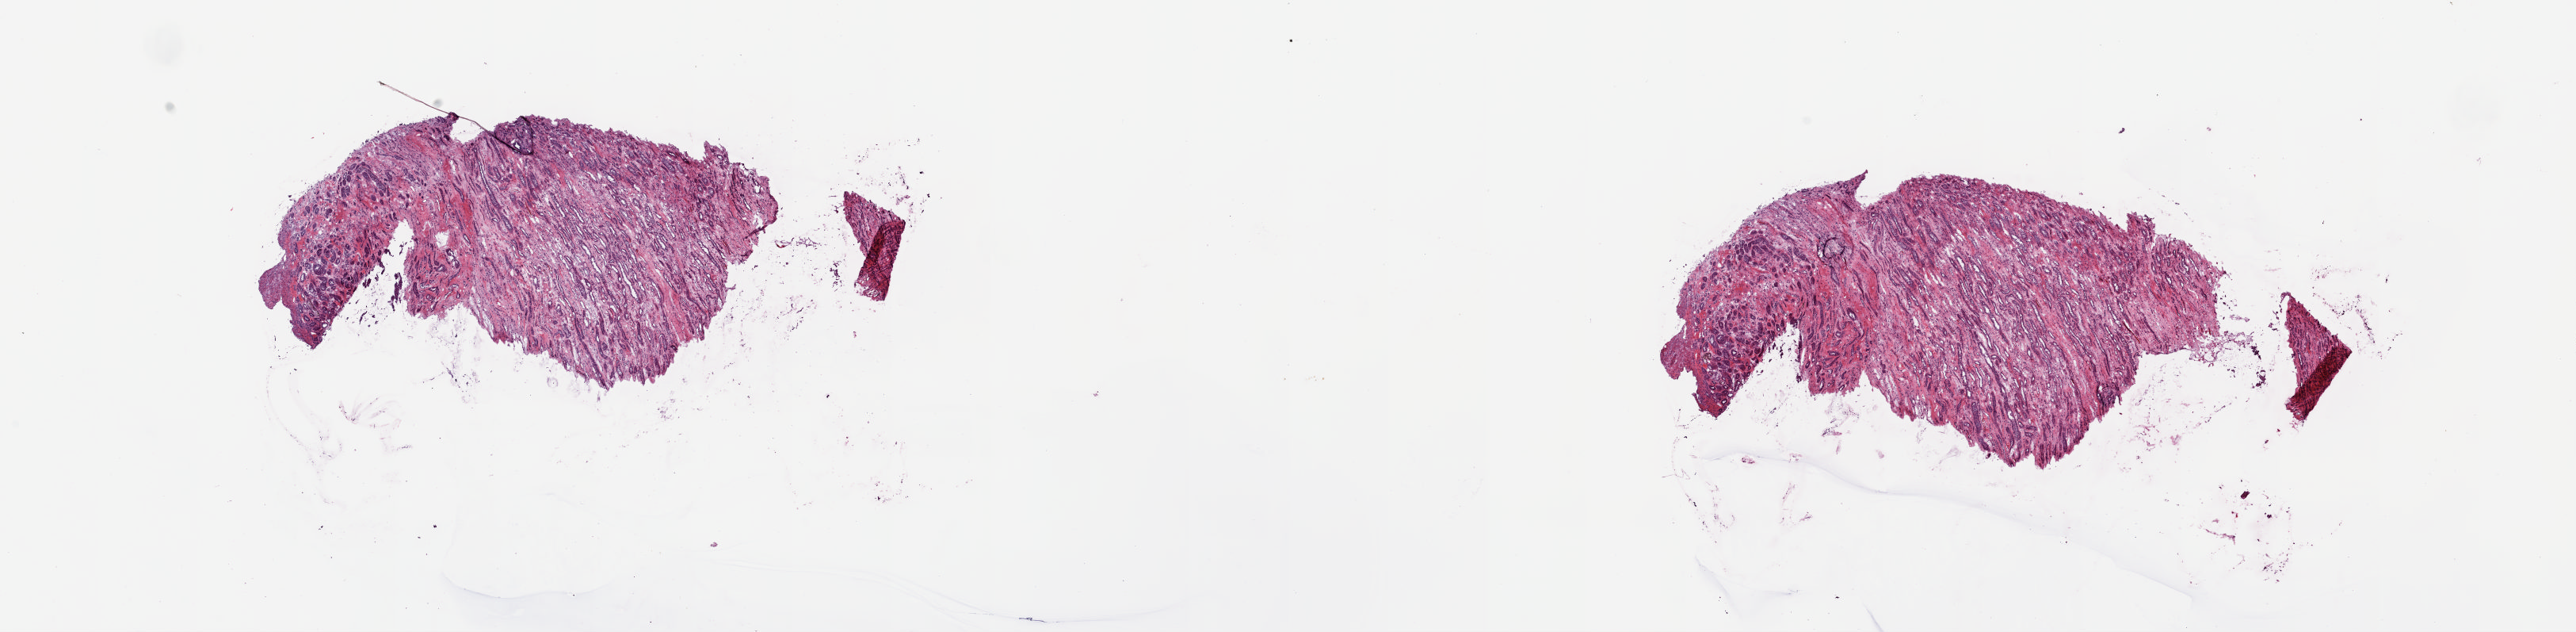
Whole-slide histology image, Hematoxylin and eosin (H&E) stained, a low-resolution overview of the entire scanned area, about 25.8 x 6.3 mm; frozen section from the top of the tissue portion; solid tissue normal (non-tumour tissue) sample from the kidney. Patient: male, age at initial diagnosis 74 years. Pathologist review of this section (percent, as recorded): tumour cells 0%, tumour nuclei 0%, normal cells 55%, stromal cells 45%, necrosis 0%. Infiltration values recorded for this section: lymphocyte infiltration 0%, monocyte infiltration 0%, neutrophil infiltration 0%.
This section: solid tissue normal (non-tumour) sample from the same patient. Patient diagnosis: Papillary adenocarcinoma, NOS.